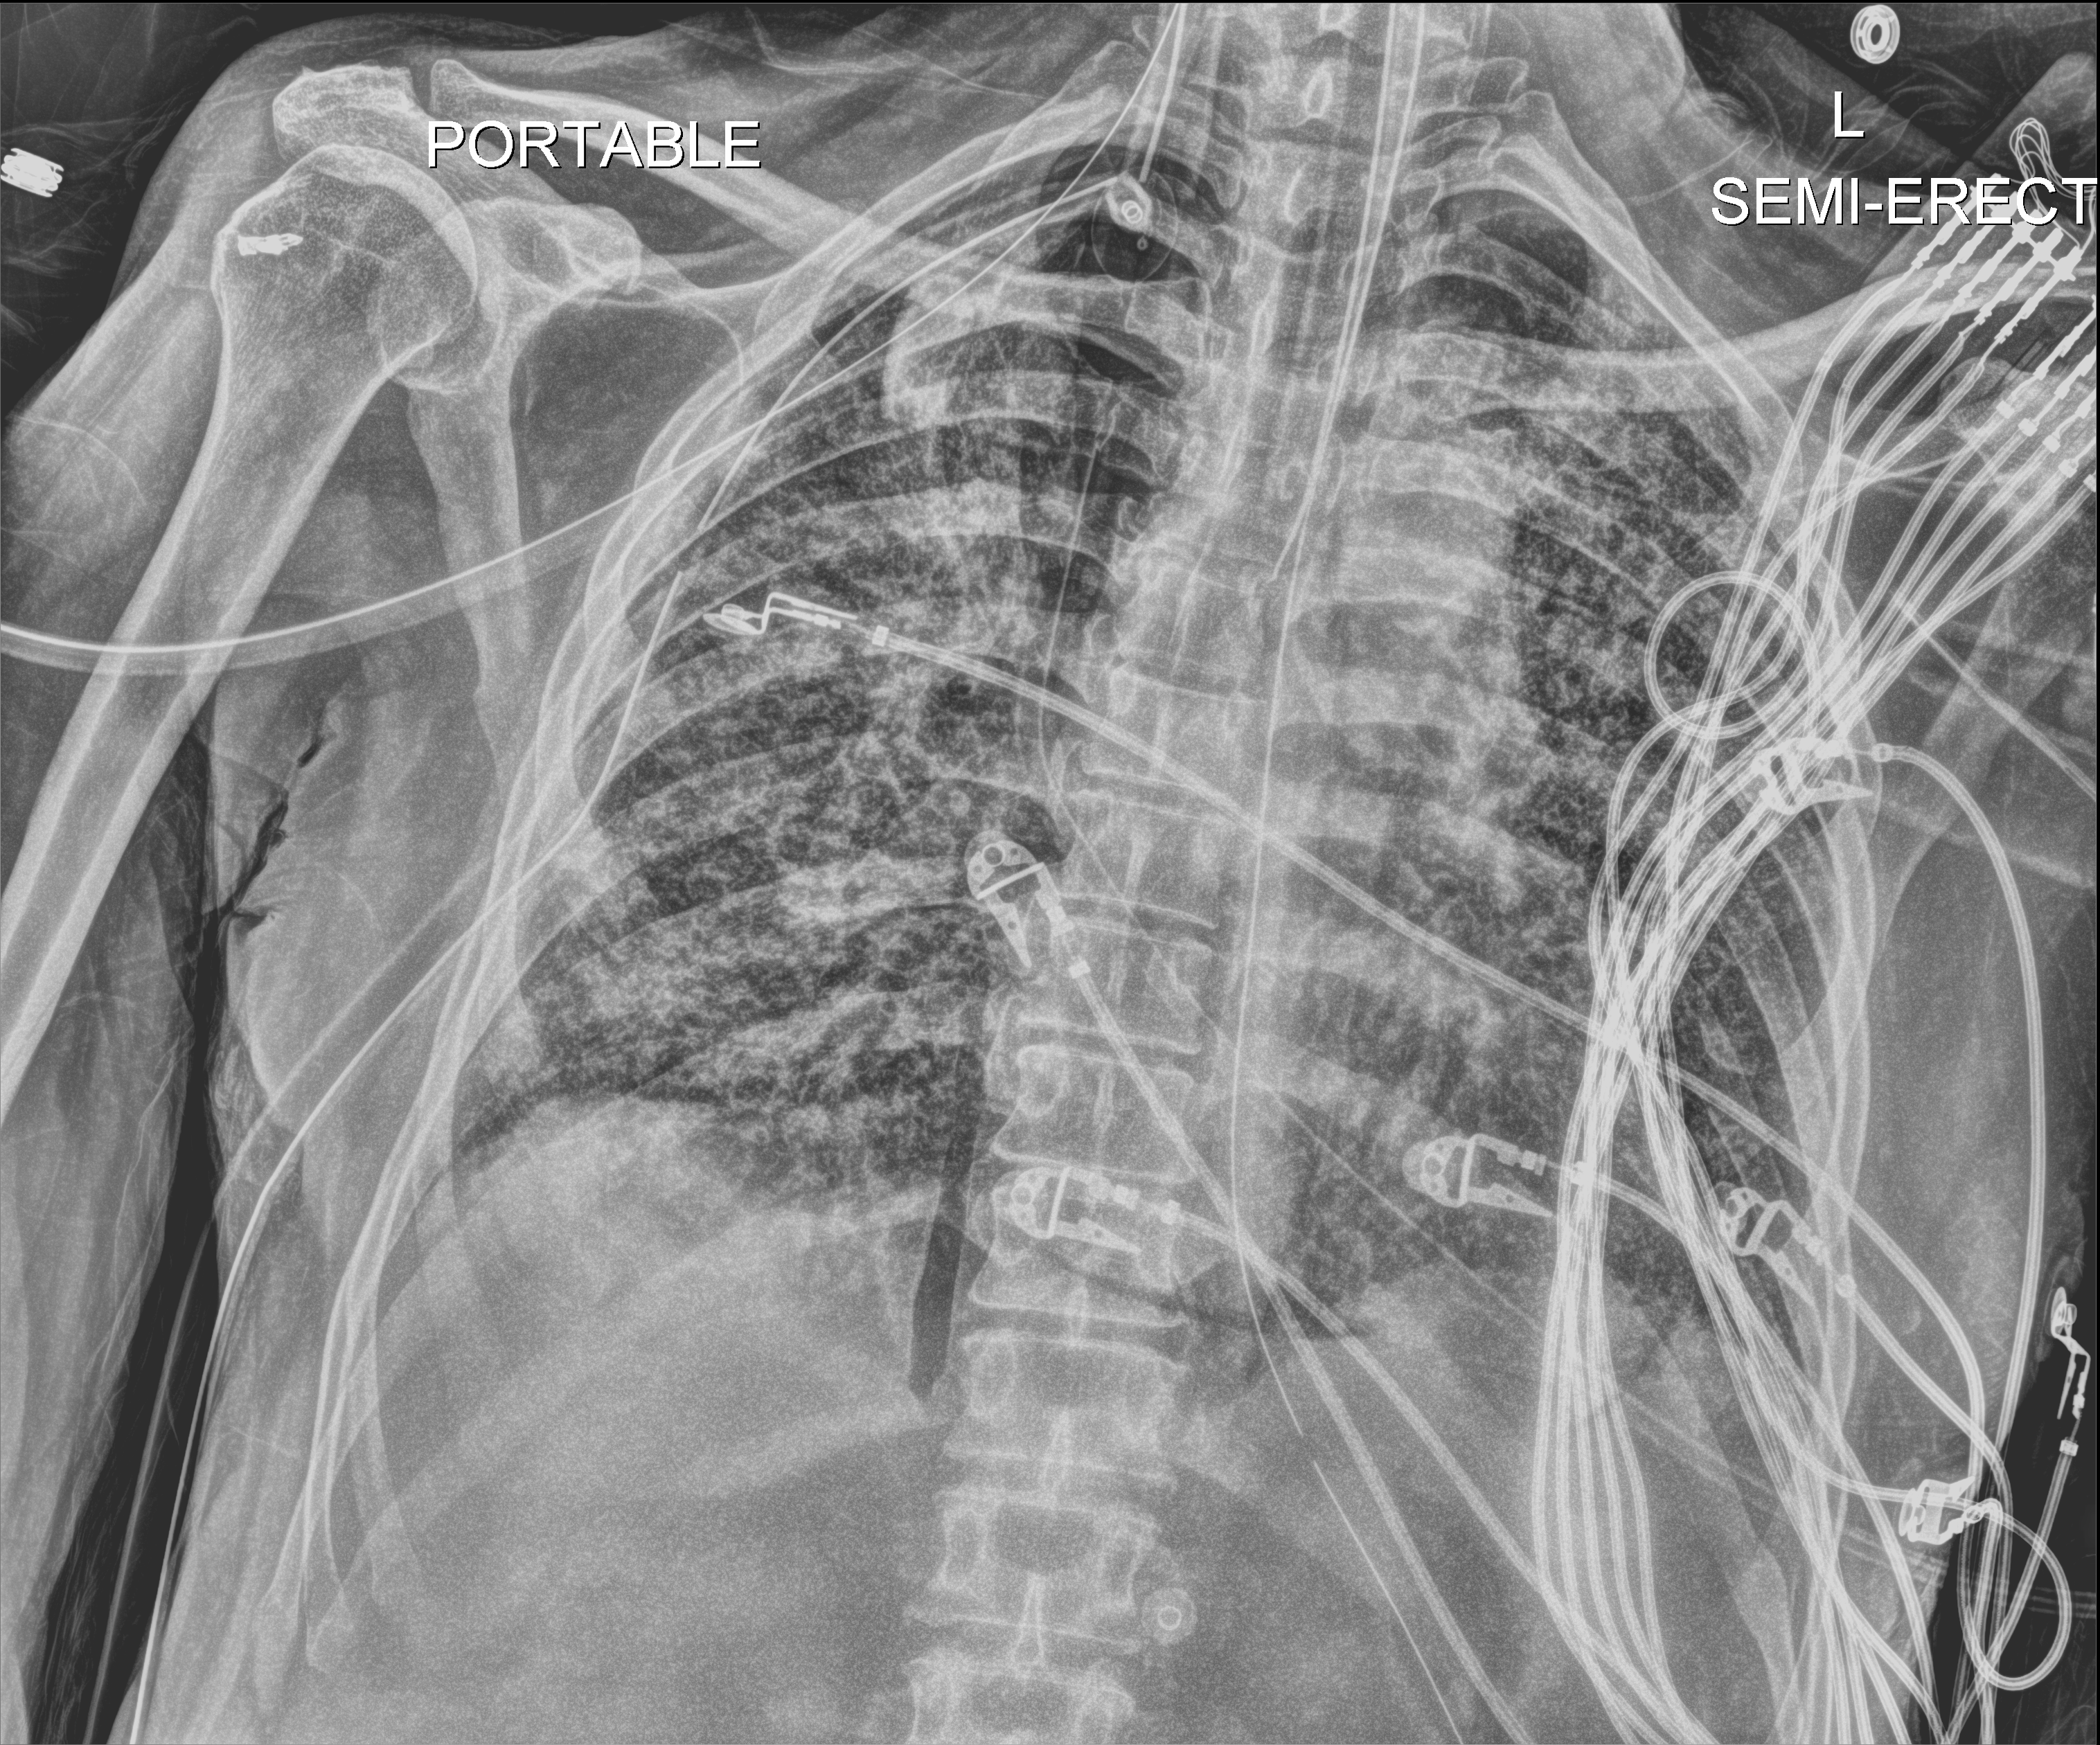
Chest X-ray (portable); anteroposterior (AP) projection. Patient hospitalised with COVID-19; male, aged 60–74 years.
From the hospital-stay record, not from the radiograph (when in the stay this image was taken is not recorded): mechanically ventilated during this hospital stay: yes; other chronic lung disease (admission record): yes; admitted to intensive care during this hospital stay: yes.